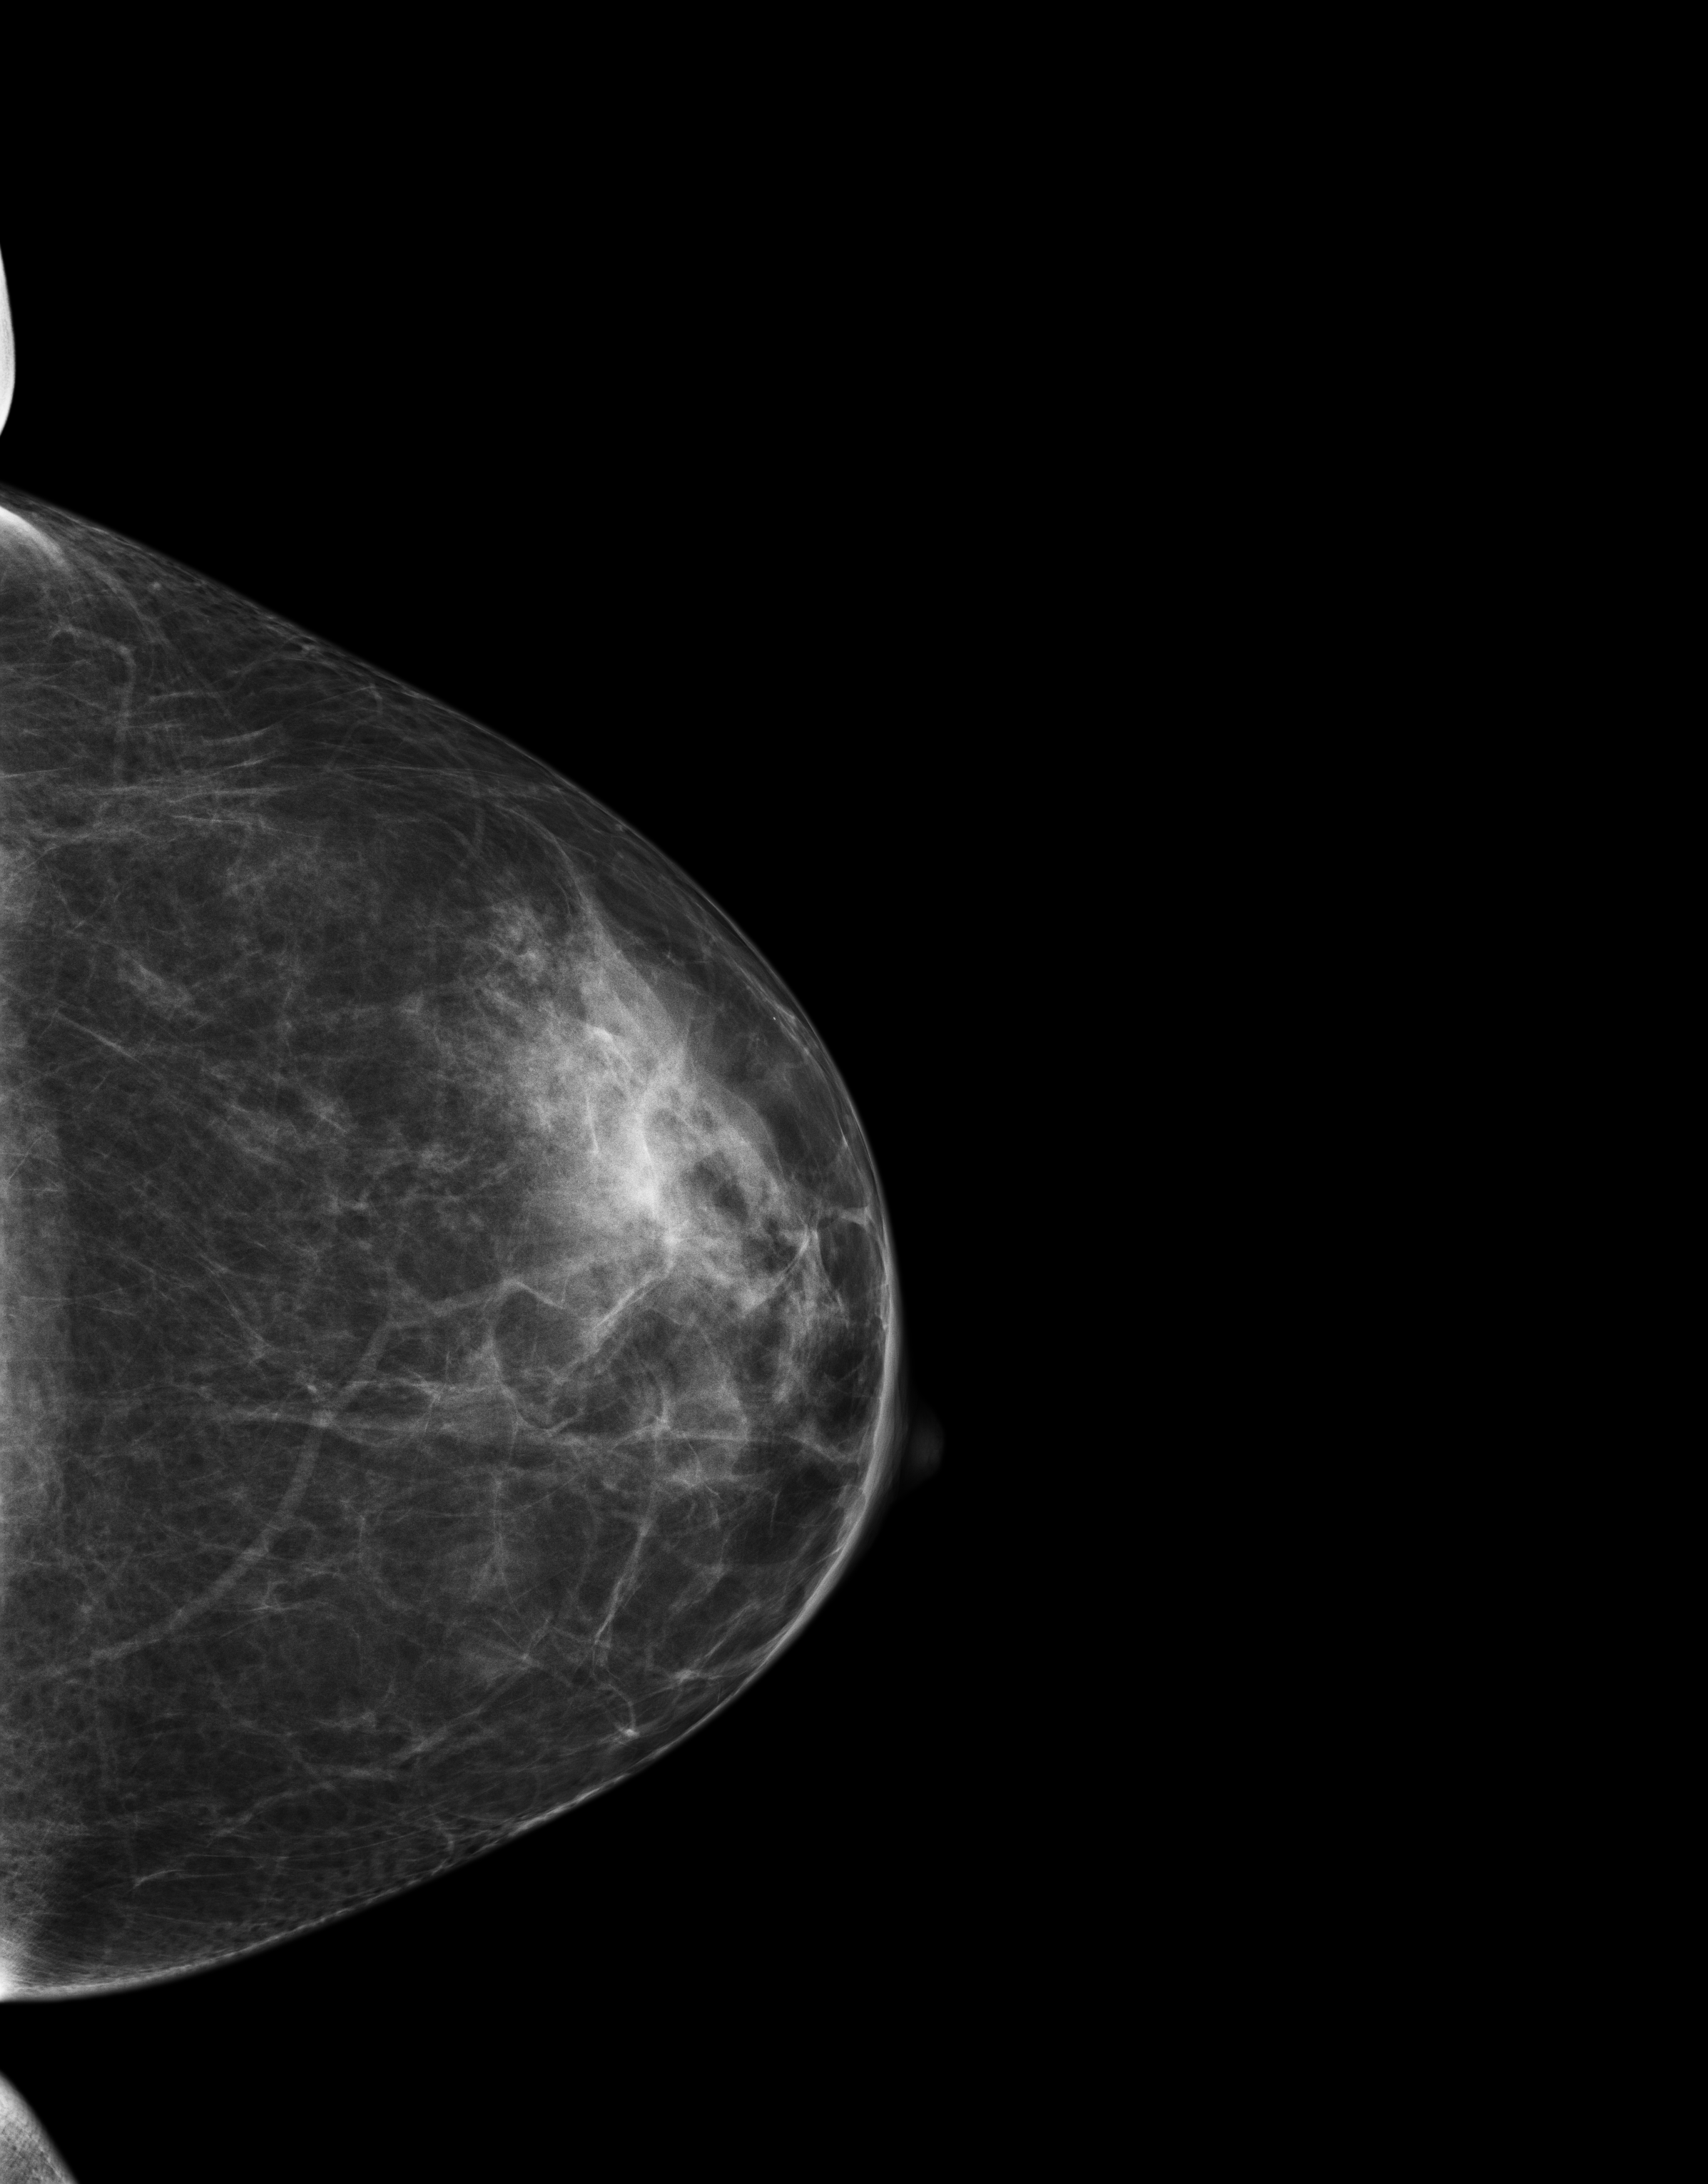
Full-field digital mammogram (FFDM); left breast; craniocaudal (CC) view; annual screening mammography examination; compressed breast thickness 60 mm; system: Senographe Essential ADS_56.21.3. Female patient, age 48 years.
- BI-RADS breast density category at the screening exam (both breasts, scale 1–4): 3
- final BI-RADS assessment for this screening round (tomosynthesis exam, both breasts): category 2
- recall: no recall after this screen